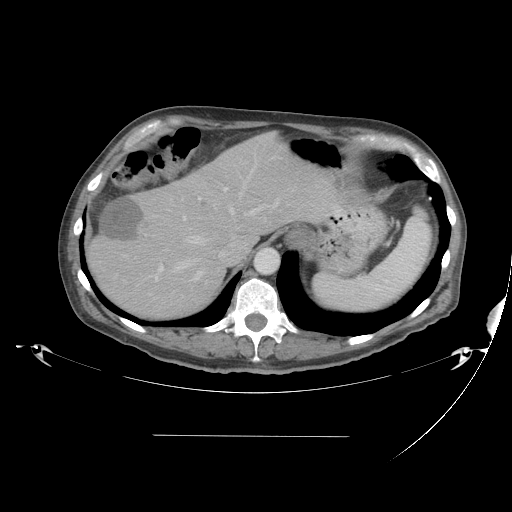
Contrast-enhanced abdominal CT, one axial slice; position 33 of 48 along the scan axis; 120 kVp; intravenous contrast given; soft-tissue window (W 400 / L 40 HU); 5 mm slice thickness; 512 × 512 image matrix, field of view 486 × 486 mm. Male patient, age 65 years. From the clinical record (not read from this slice): diagnosis: colorectal cancer liver metastases, imaged before liver resection; multiple liver metastases: yes; largest metastasis: 11 cm; chemotherapy before resection: yes.
Structures marked on this image (expert manual segmentation):
- hepatic veins: bounding box (x1, y1, x2, y2) in pixels: (146, 154, 278, 282)
- liver: (88, 135, 333, 320)
- planned liver remnant (the part of the liver to remain after resection): (171, 135, 333, 241)
- portal vein (with intrahepatic branches): (158, 183, 265, 272)
- liver metastasis: (98, 198, 141, 239)